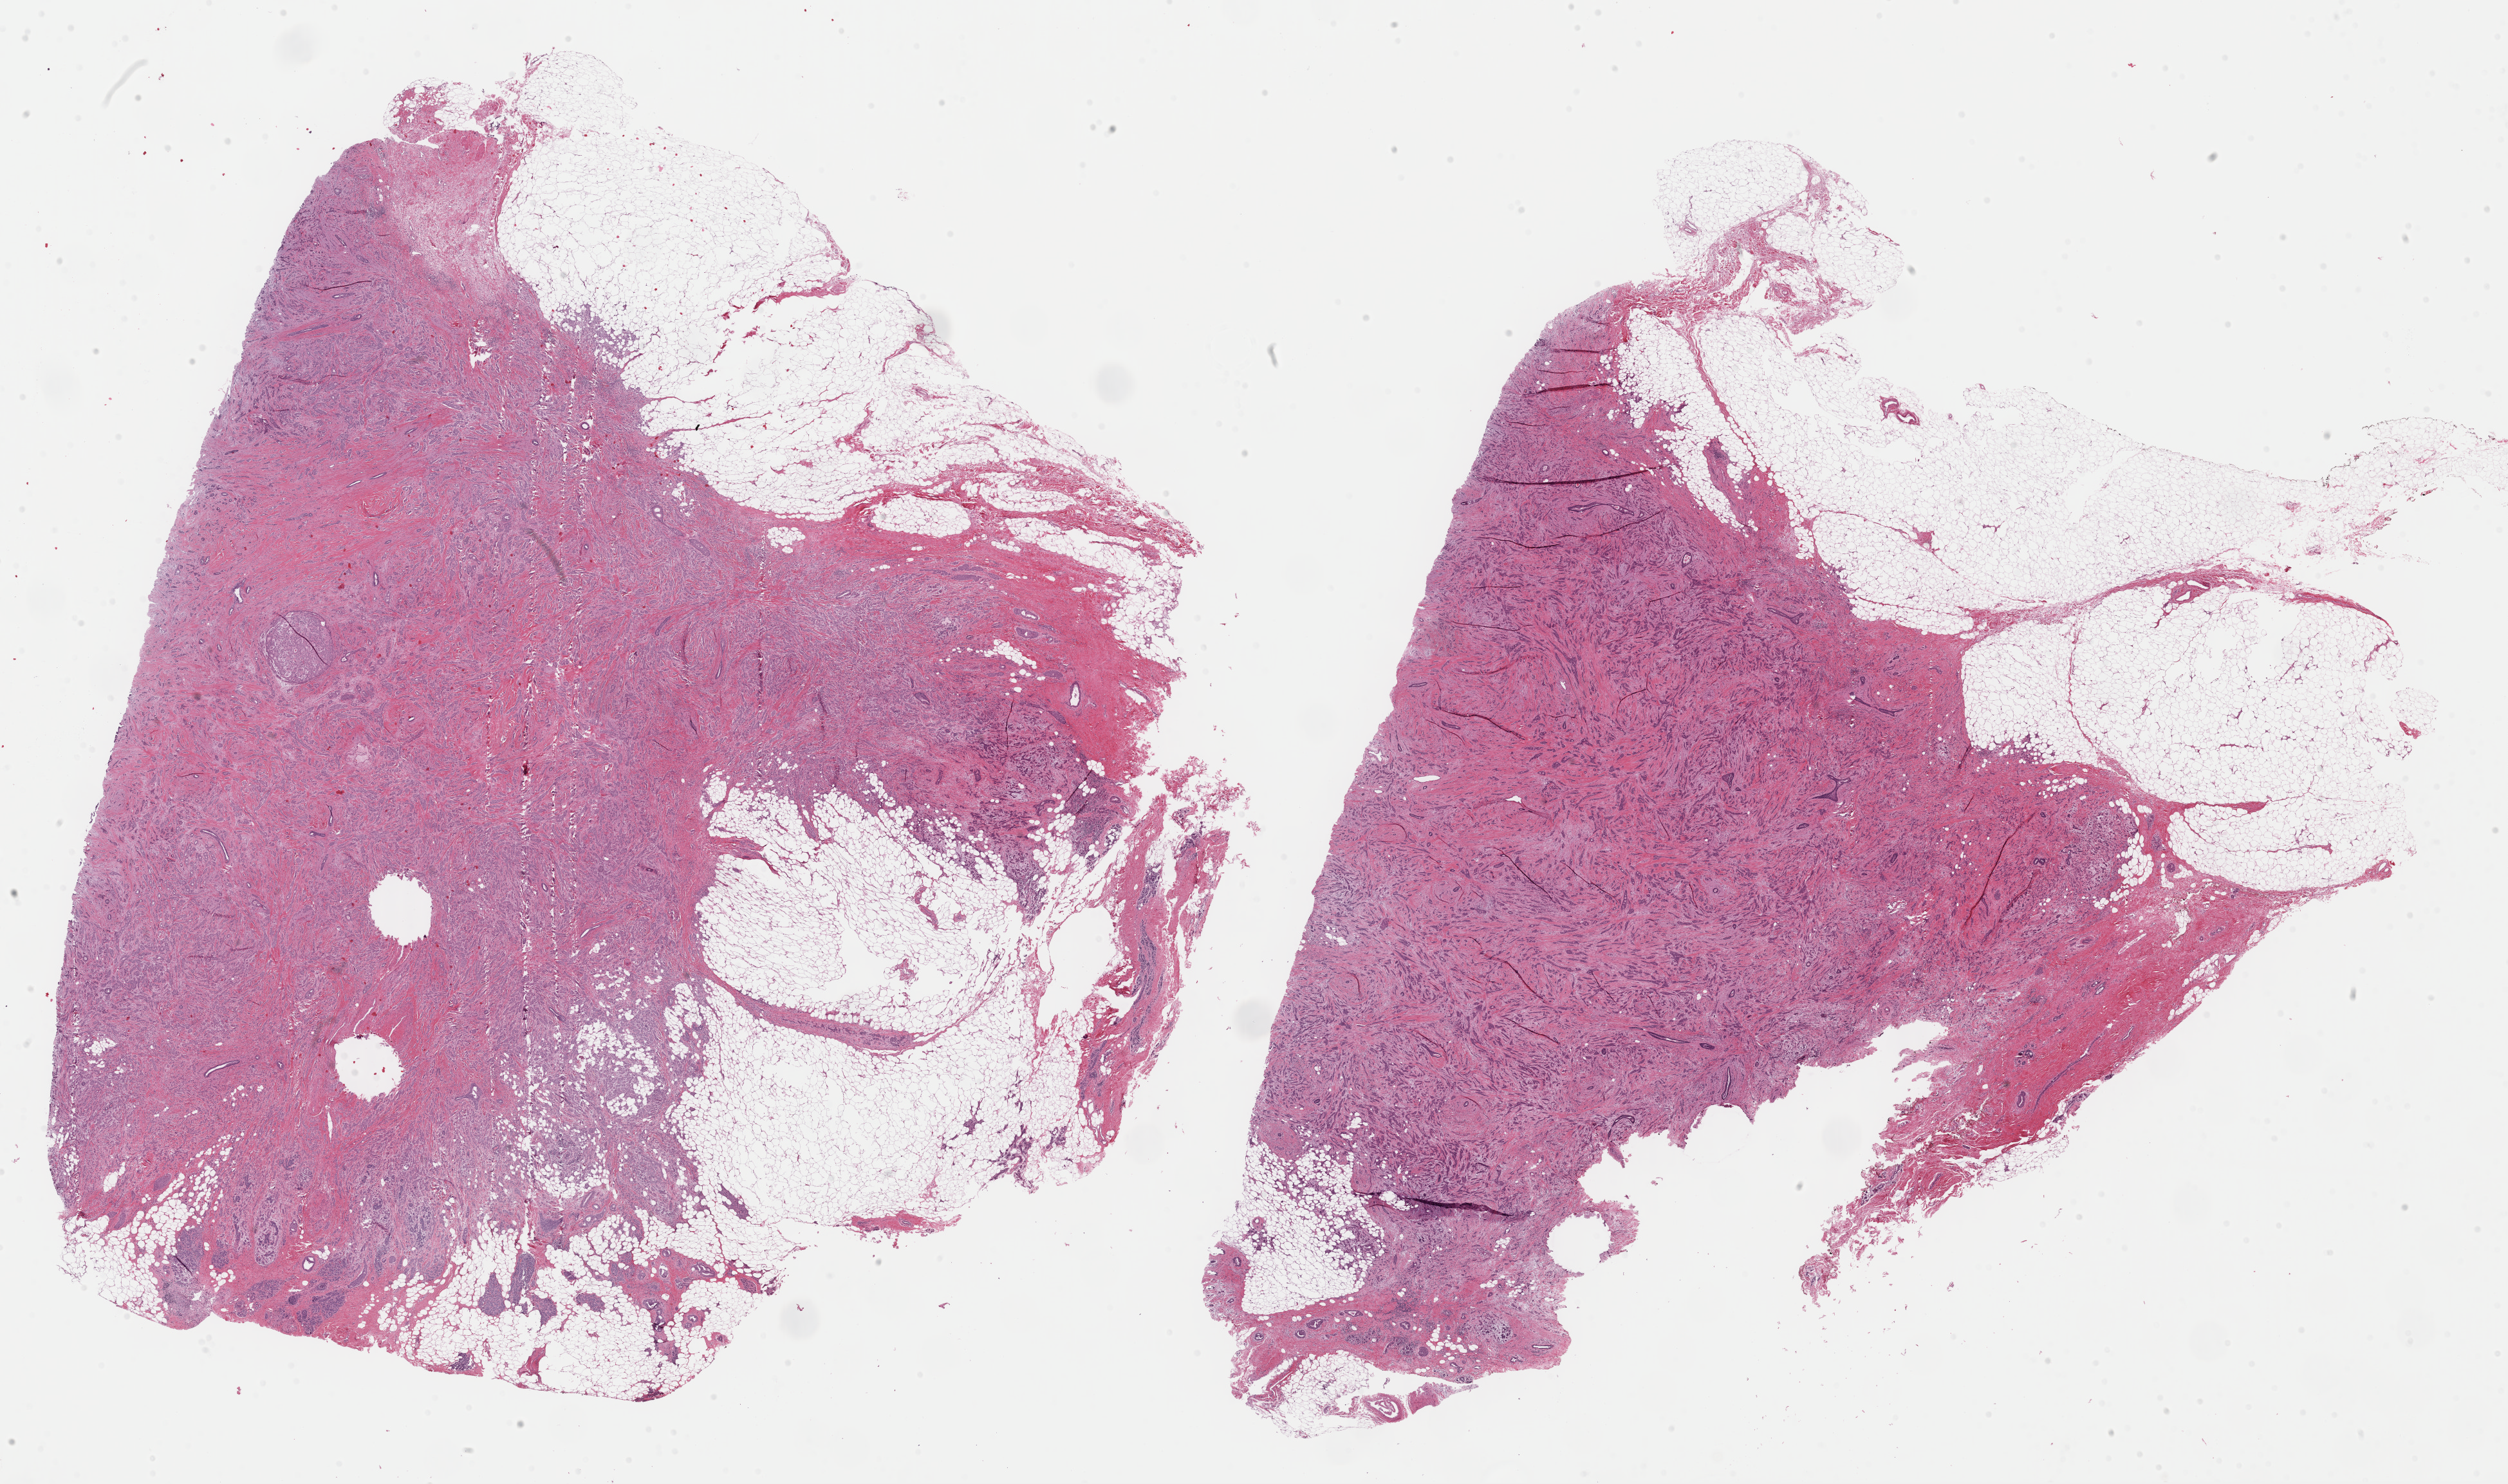
Whole-slide histology image, H&E-stained, shown as a low-resolution overview of the whole scanned area (about 30.8 x 18.2 mm); formalin-fixed paraffin-embedded (FFPE) diagnostic section; sample: primary tumour, breast. Female patient; age at initial diagnosis 38 years.
AJCC pathologic stage: IIIA (6th edition). Pathologic diagnosis: Infiltrating duct and lobular carcinoma.